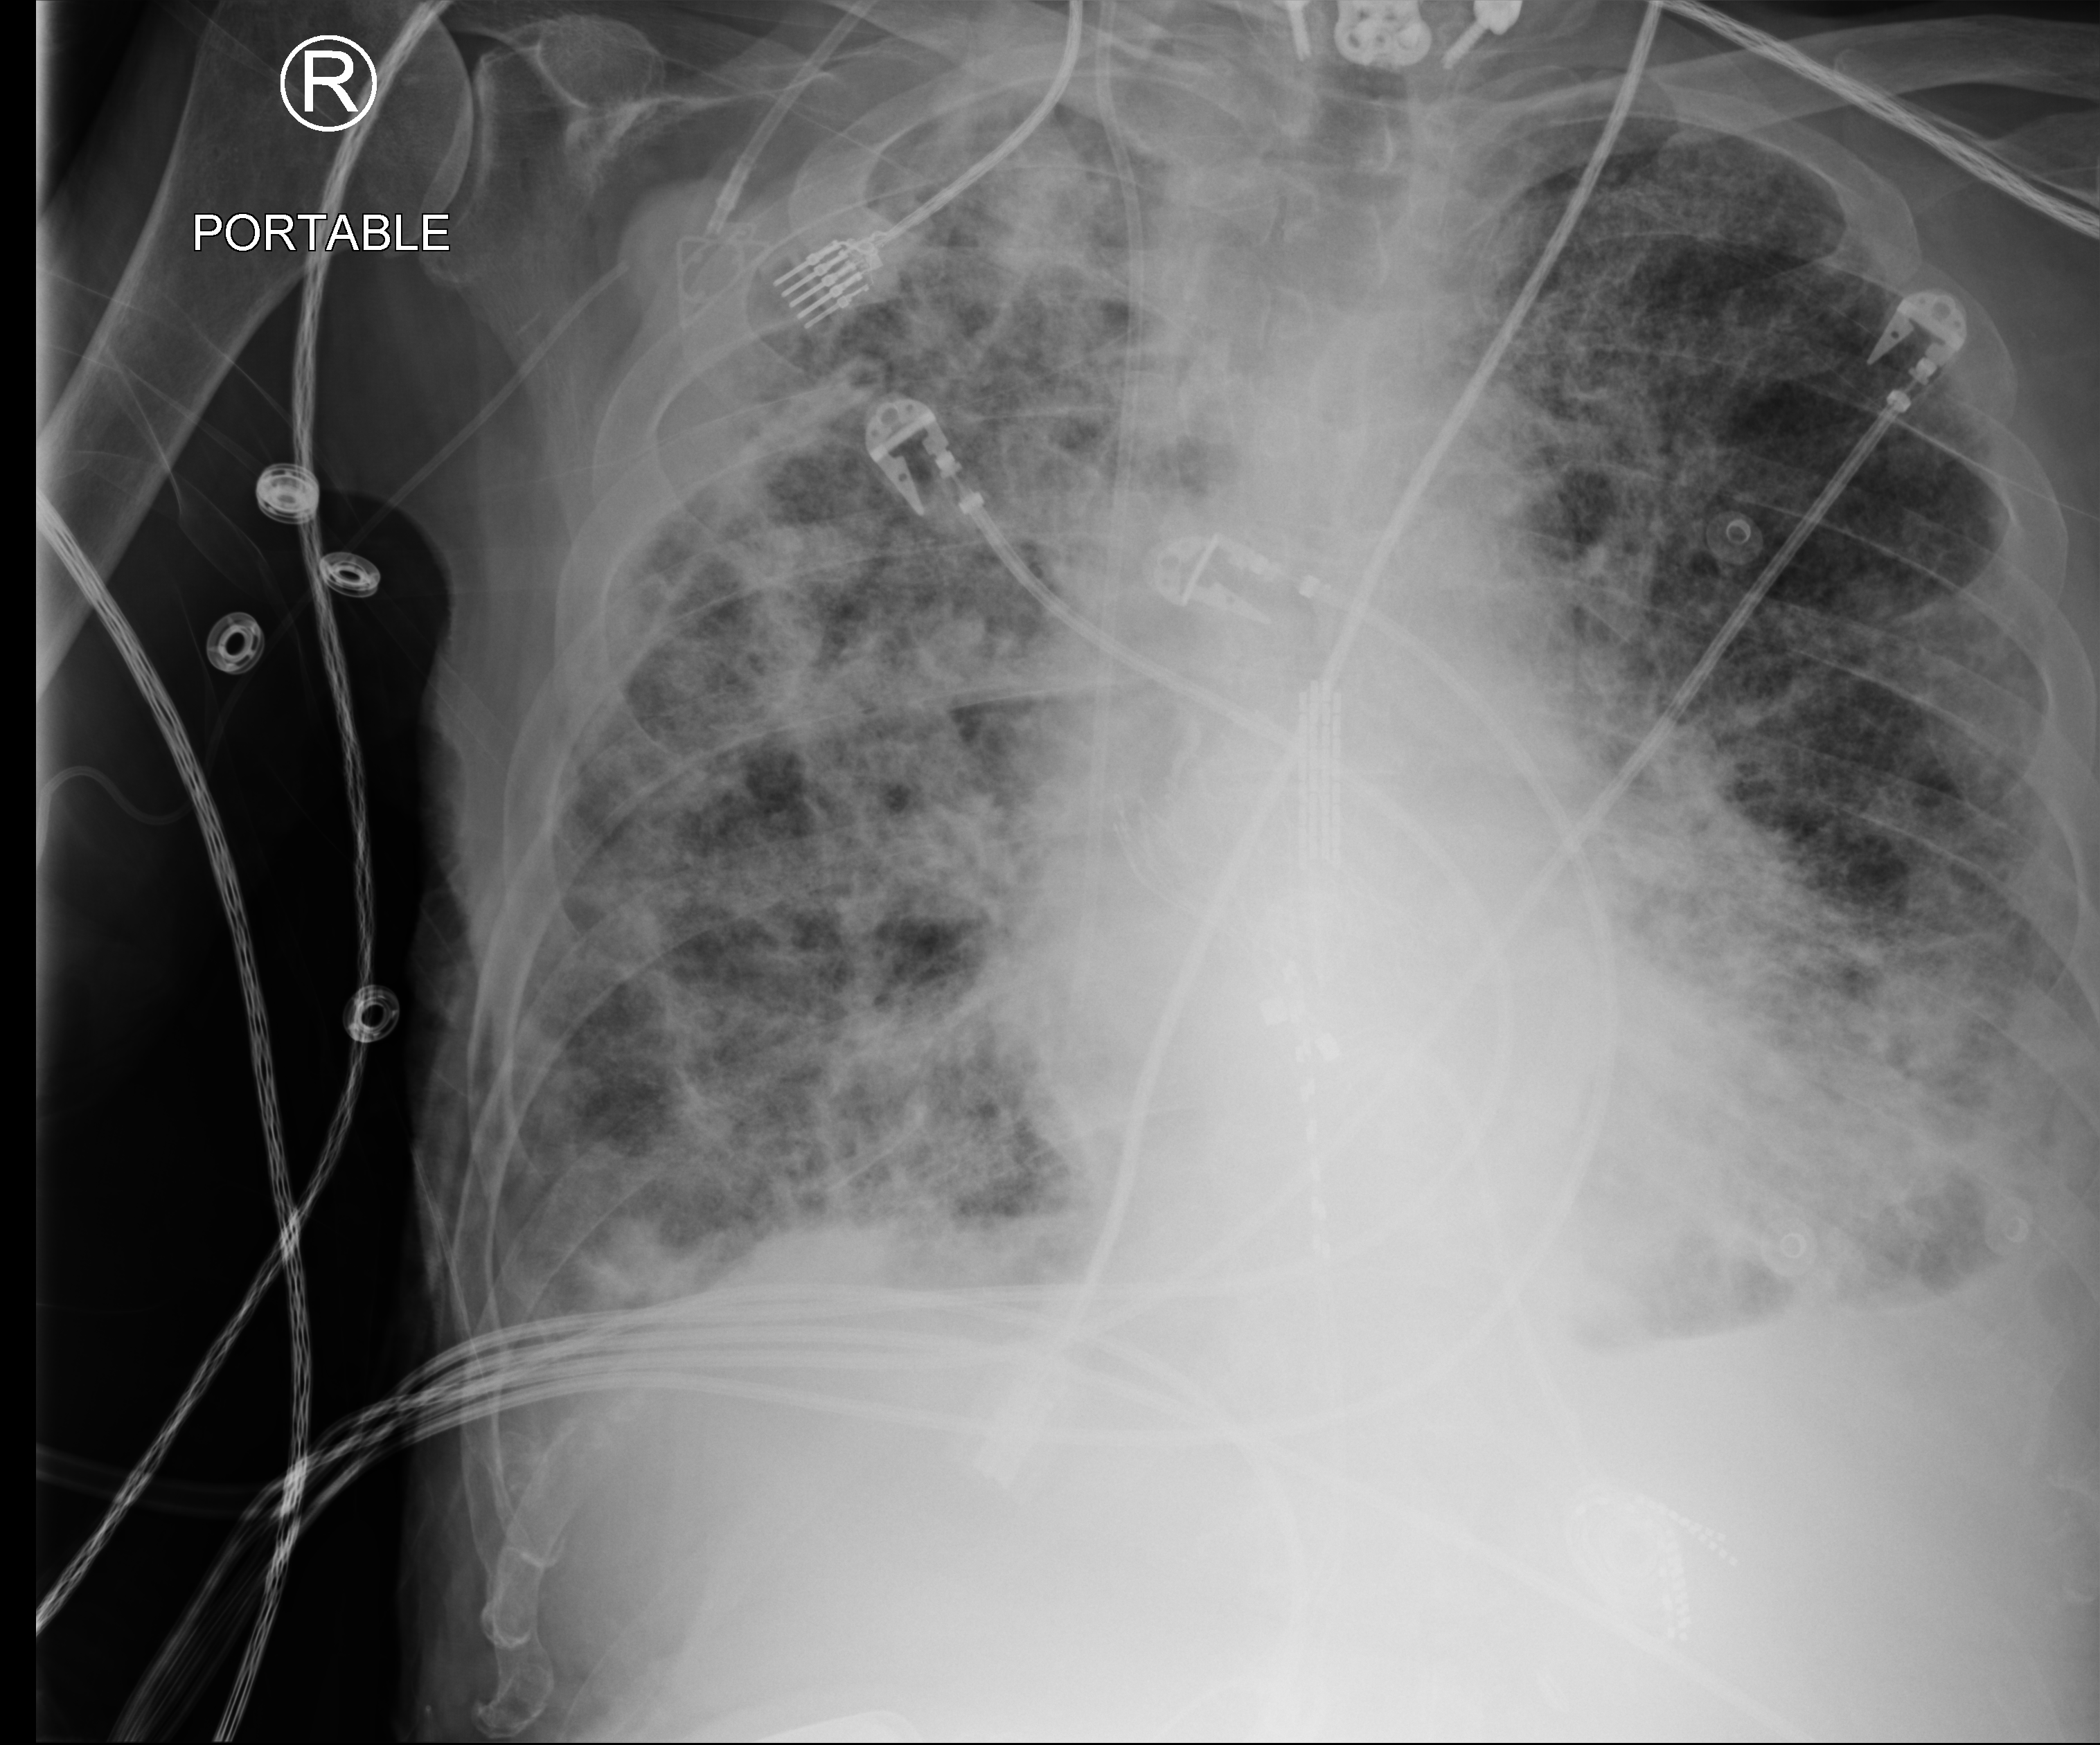
Portable chest radiograph; anteroposterior (AP) projection. Male patient hospitalised with COVID-19, age 75–90 years.
From the hospital-stay record, not from the radiograph (when in the stay this image was taken is not recorded): hypertension (admission record): yes.